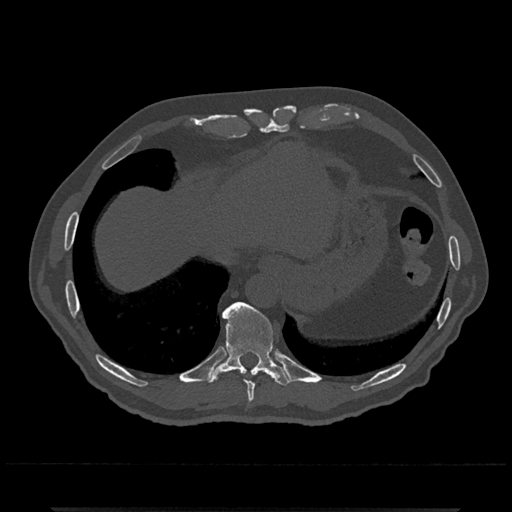
CT including the spine, one axial slice; slice 573 of 797 in the series (ordered by position); reconstruction kernel Br40s/3; 120 kVp; bone window (W 1800 / L 400 HU); 0.5 mm slice thickness; 512 × 512 image matrix, field of view 393 × 393 mm. Male patient, age 67 years. Case-level facts recorded for this patient, not image findings: primary cancer: prostate.
Outlined on this slice (semi-automatically segmented with operator editing):
- T10 vertebra: bounding box (x1, y1, x2, y2) in pixels: (207, 302, 291, 387)
- T9 vertebra: (245, 380, 255, 403)